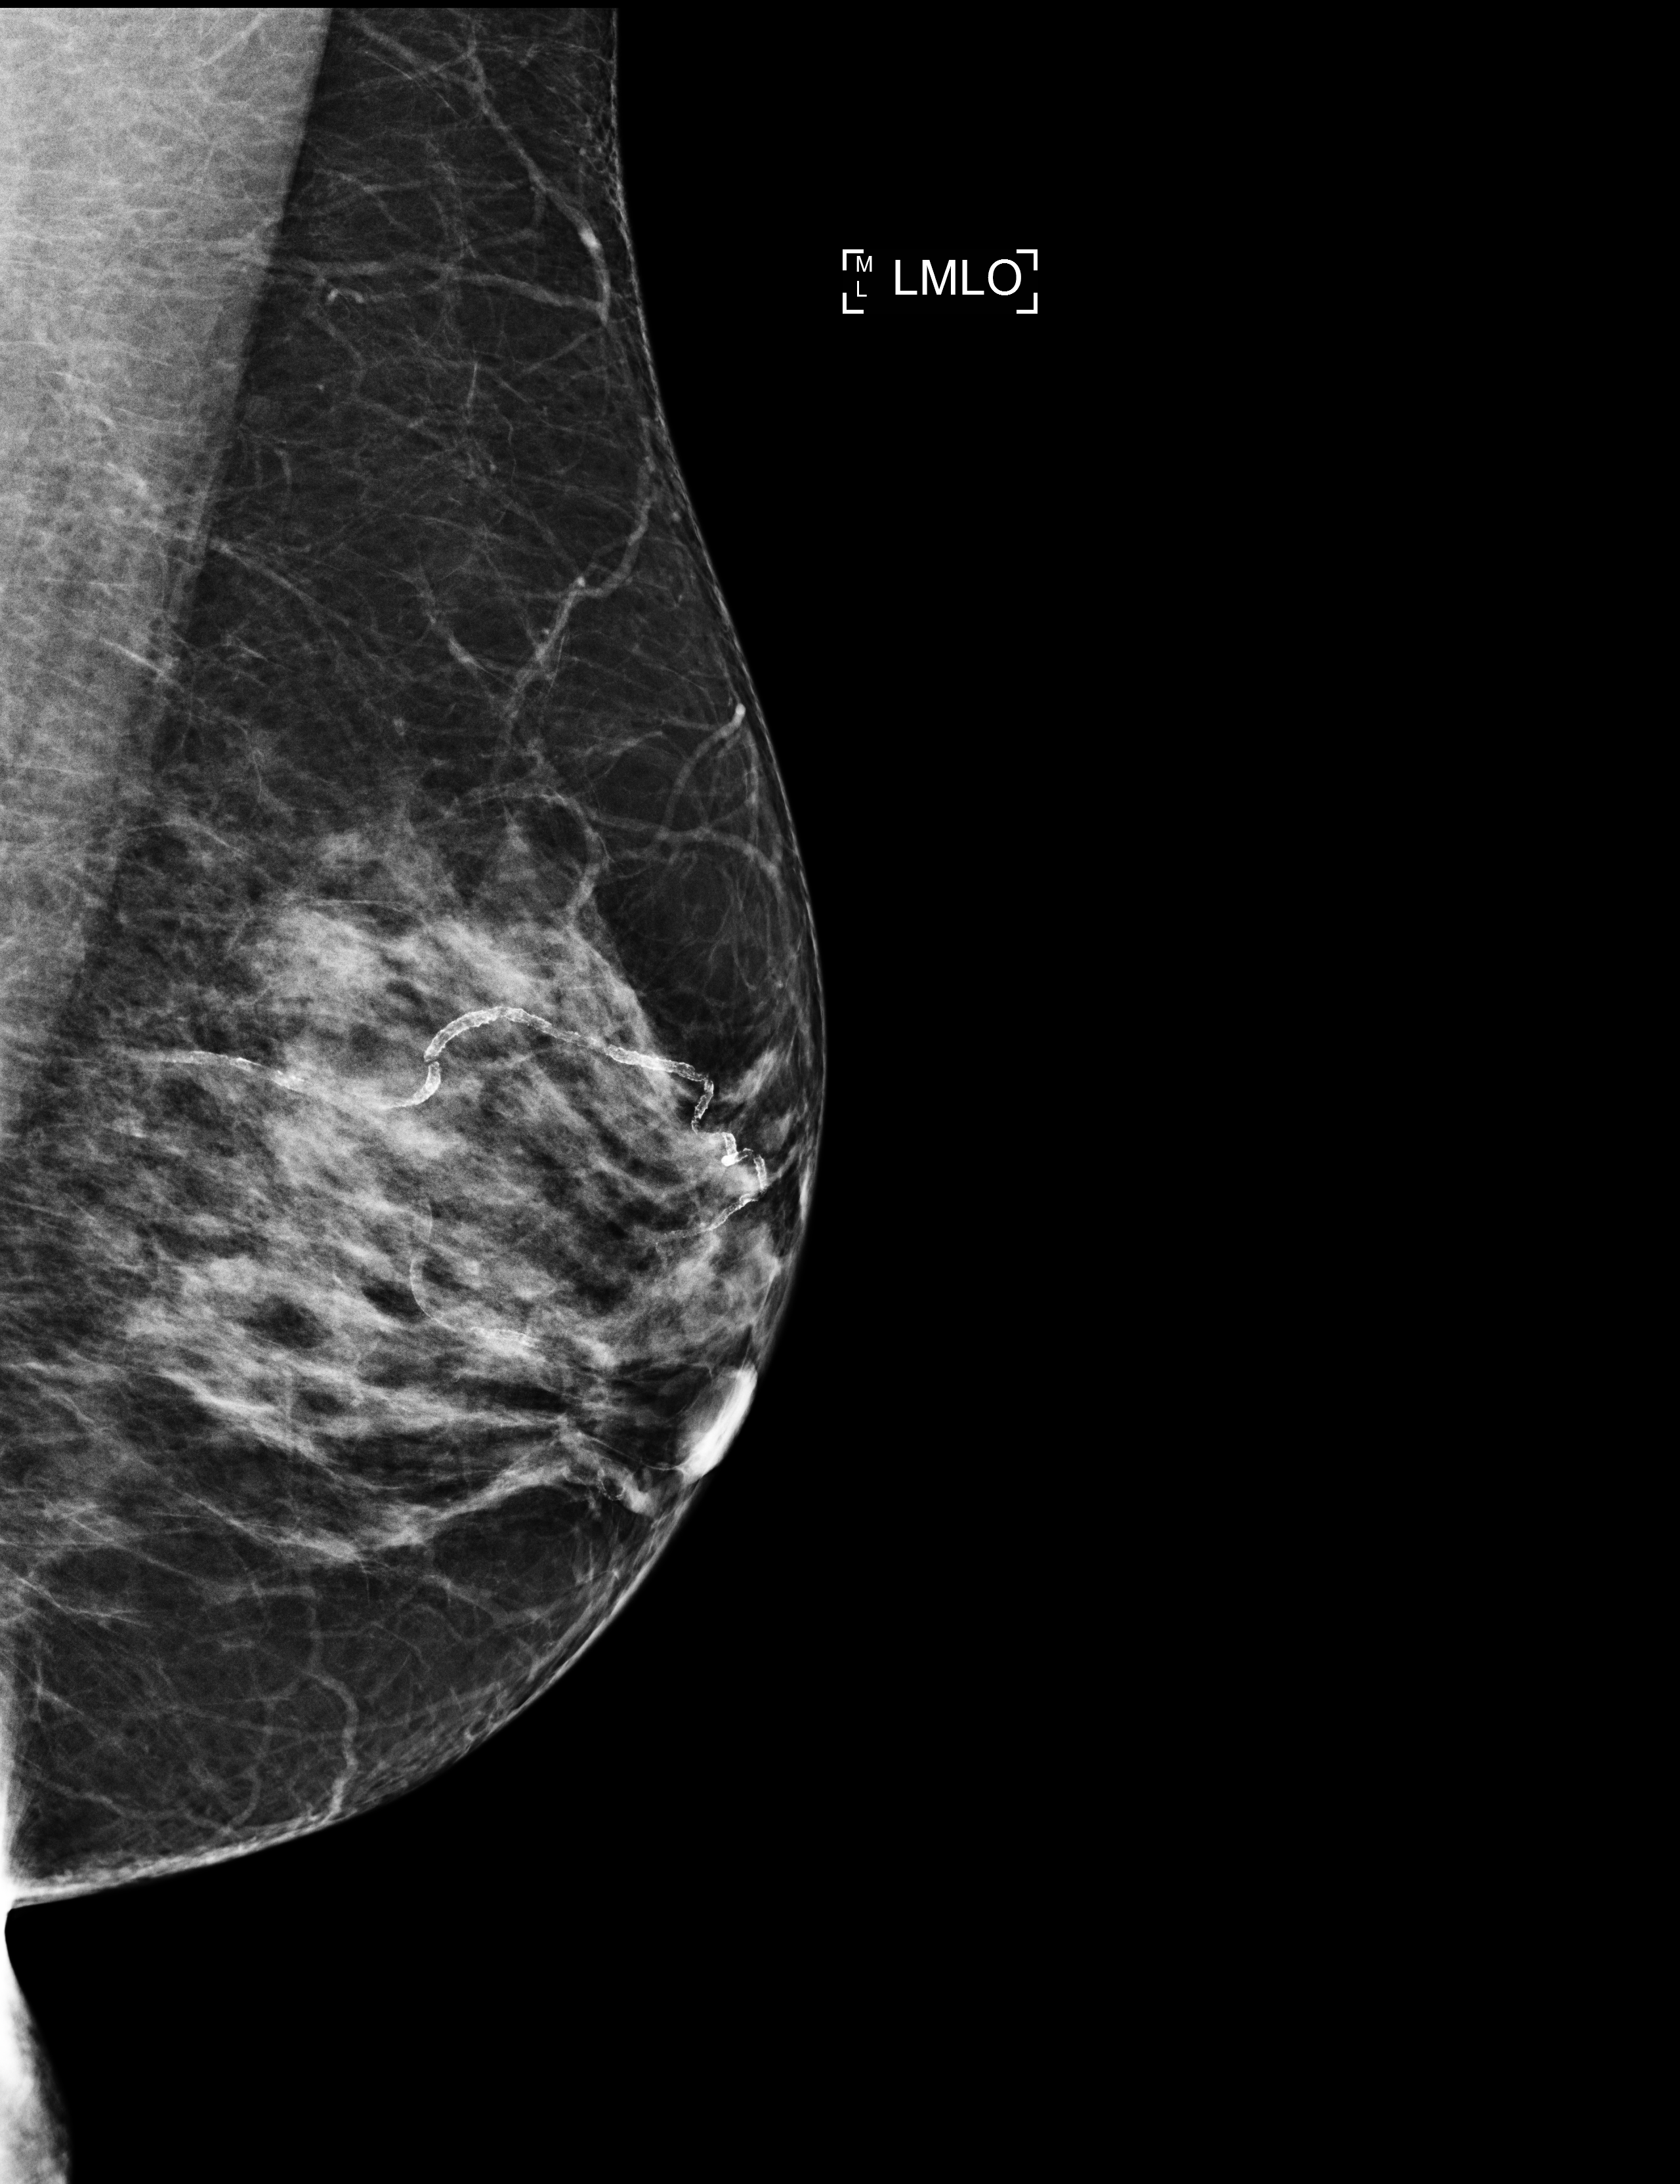
Annual screening mammography examination, system: Selenia Dimensions. Patient aged 60 years (female).
Image type: full-field digital mammogram. Breast: left. Projection: MLO view.